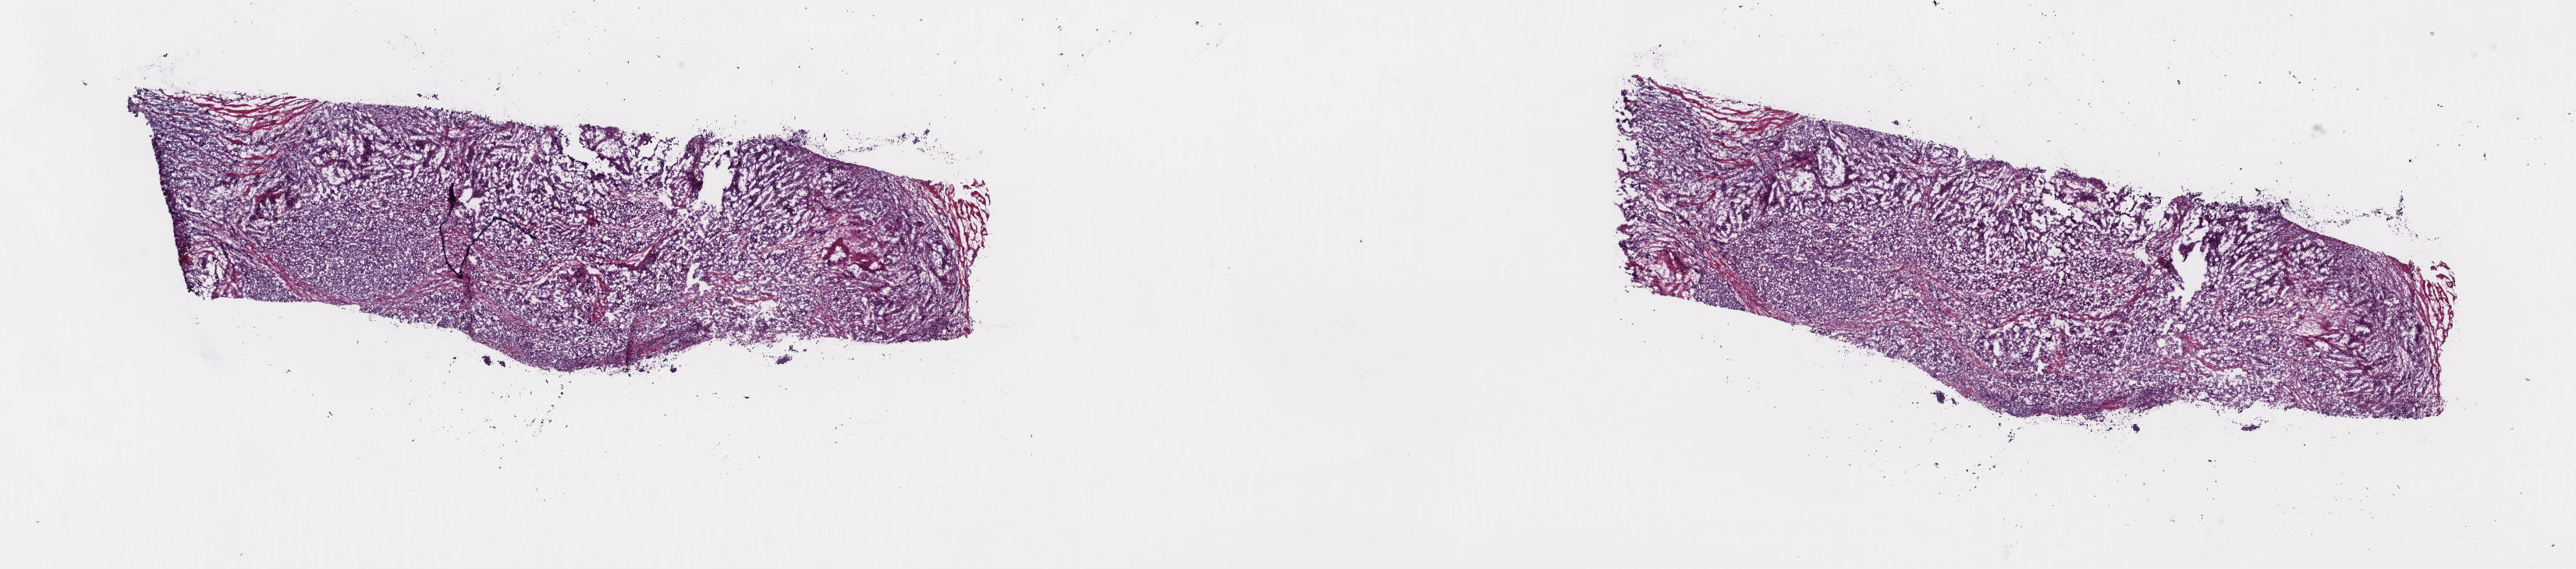
Whole-slide histology image, H&E-stained, a low-resolution overview of the entire scanned area, about 26.1 x 5.8 mm (from a 40x scan), frozen section from the top of the tissue portion, esophagus, primary tumour sample. Male patient; age at initial diagnosis 44 years. Histologic grade: G2 (moderately differentiated). Slide review estimates, as recorded: tumour cells 80%, tumour nuclei 80%, normal cells 0%, stromal cells 19%, necrosis 1%. Inflammatory infiltration, as recorded: lymphocyte infiltration 5%, monocyte infiltration 1%, neutrophil infiltration 1%.
- diagnosis: Squamous cell carcinoma, NOS (middle third of esophagus)
- AJCC pathologic stage: IIA (6th edition)